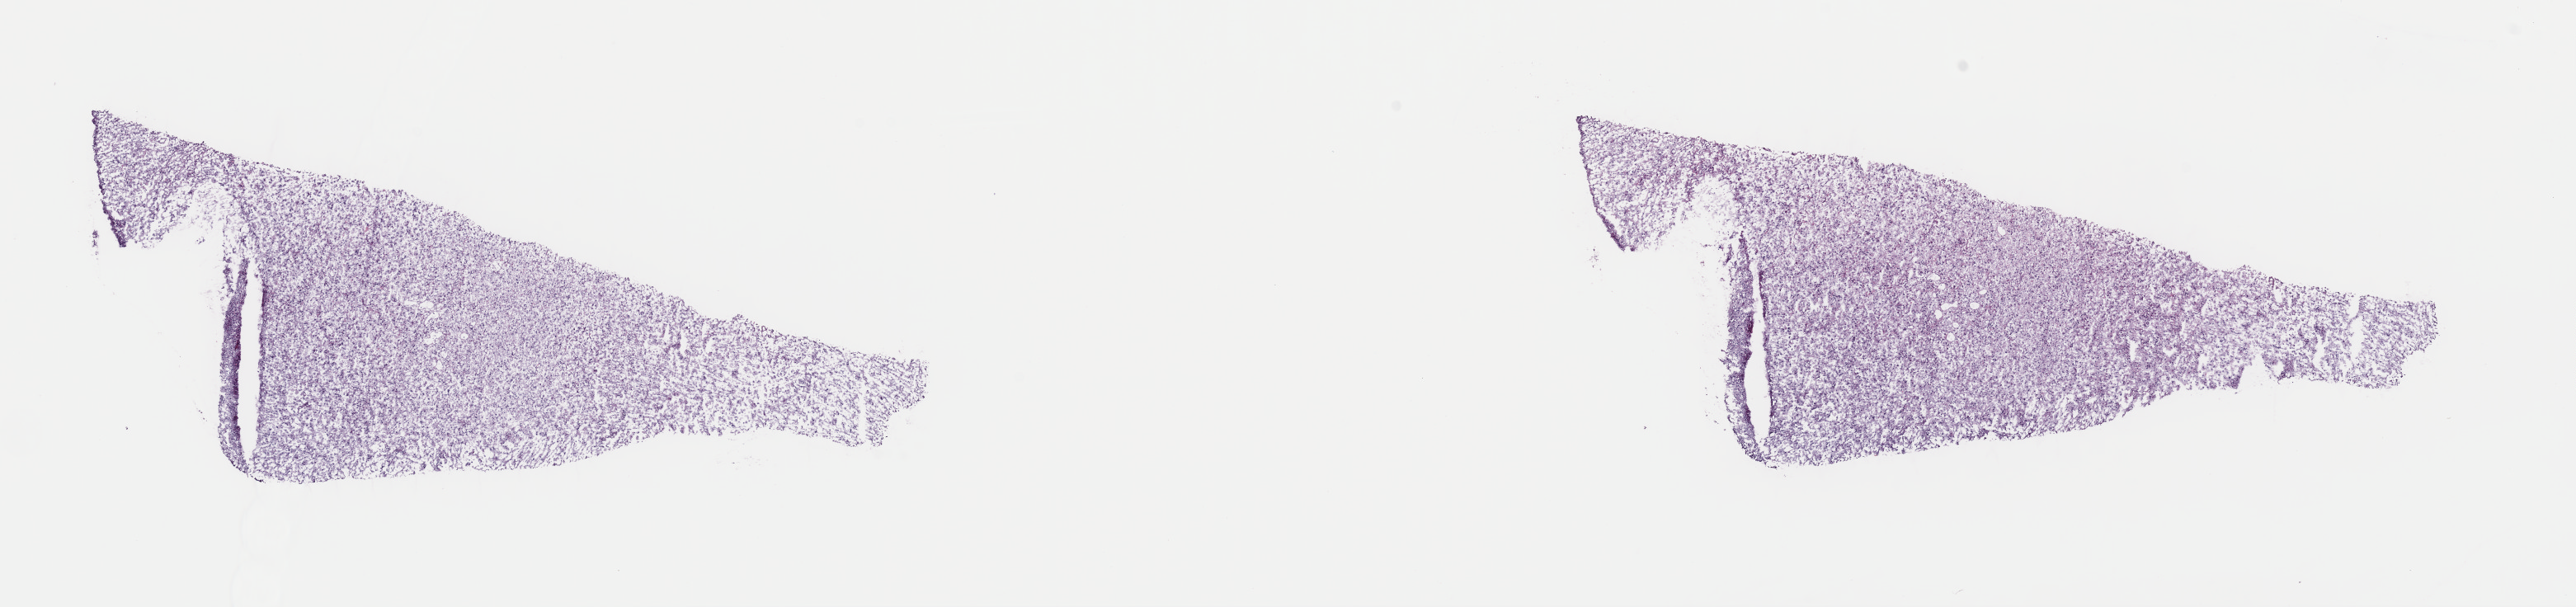
Whole-slide histology image, Hematoxylin and eosin (H&E) stained, low-resolution overview of the scanned area, about 24.7 x 5.8 mm (slide scanned at 40x), frozen section from the top of the tissue portion, brain, primary tumour sample. Patient: female, age at initial diagnosis 43 years. Histologic grade: G3 (poorly differentiated). Slide review estimates, as recorded: tumour cells 65%, tumour nuclei 90%, normal cells 15%, stromal cells 20%, necrosis 0%. Infiltration values recorded for this section: lymphocyte infiltration 0%, monocyte infiltration 0%, neutrophil infiltration 0%.
Histologic diagnosis: Astrocytoma, anaplastic (cerebrum).